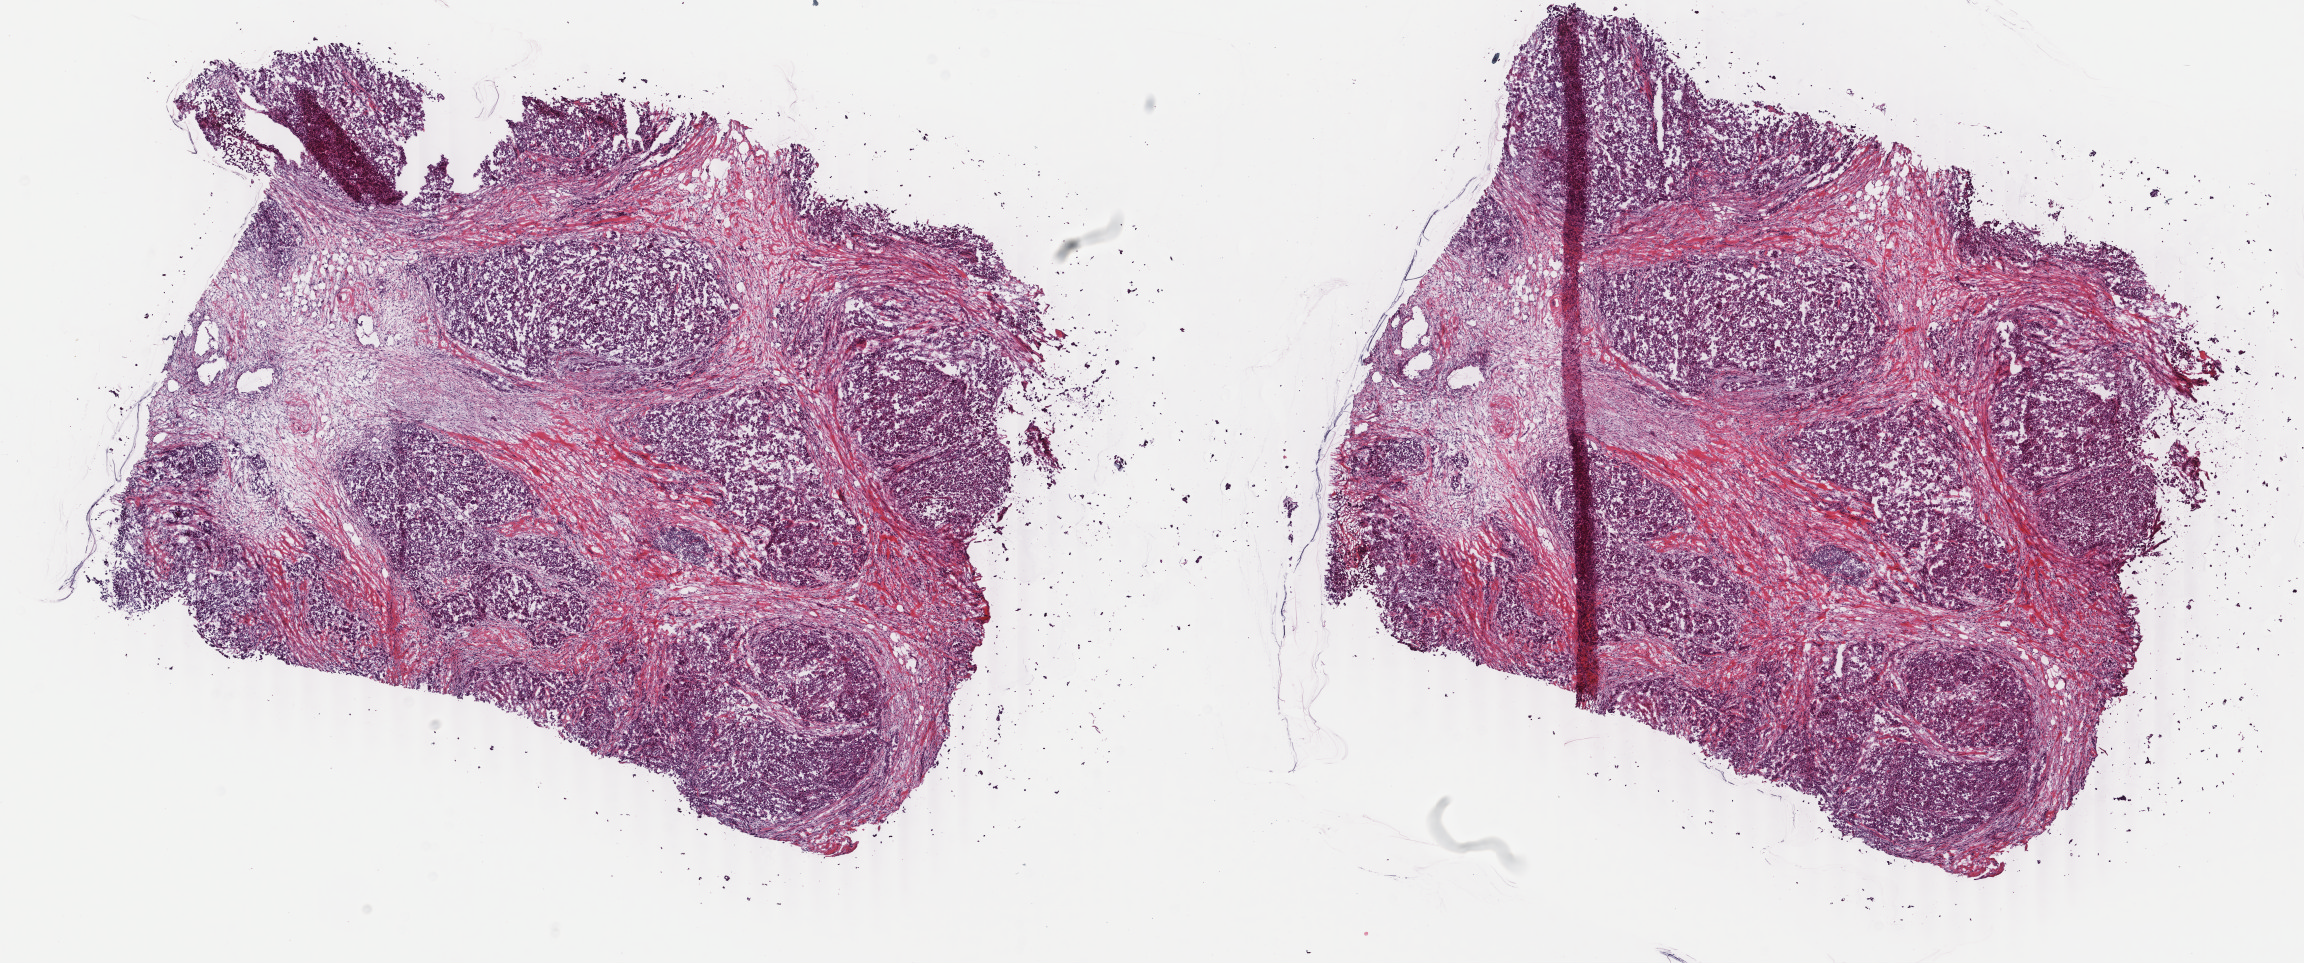
Digitized H&E-stained tissue section (whole slide) — a low-resolution overview of the entire scanned area, about 18.3 x 7.7 mm (acquisition: 40x scan), frozen section from the bottom of the tissue portion, sample: primary tumour, breast. Female patient; age at initial diagnosis 53 years. Pathologist review of this section (percent, as recorded): tumour cells 60%, tumour nuclei 70%, normal cells 0%, stromal cells 40%, necrosis 0%. Infiltration values recorded for this section: lymphocyte infiltration 0%, monocyte infiltration 0%, neutrophil infiltration 0%.
Lymph nodes positive (case pathology): 5 of 28 examined. Laterality: left. AJCC pathologic stage: IIIA. Diagnosis: Infiltrating duct carcinoma, NOS.